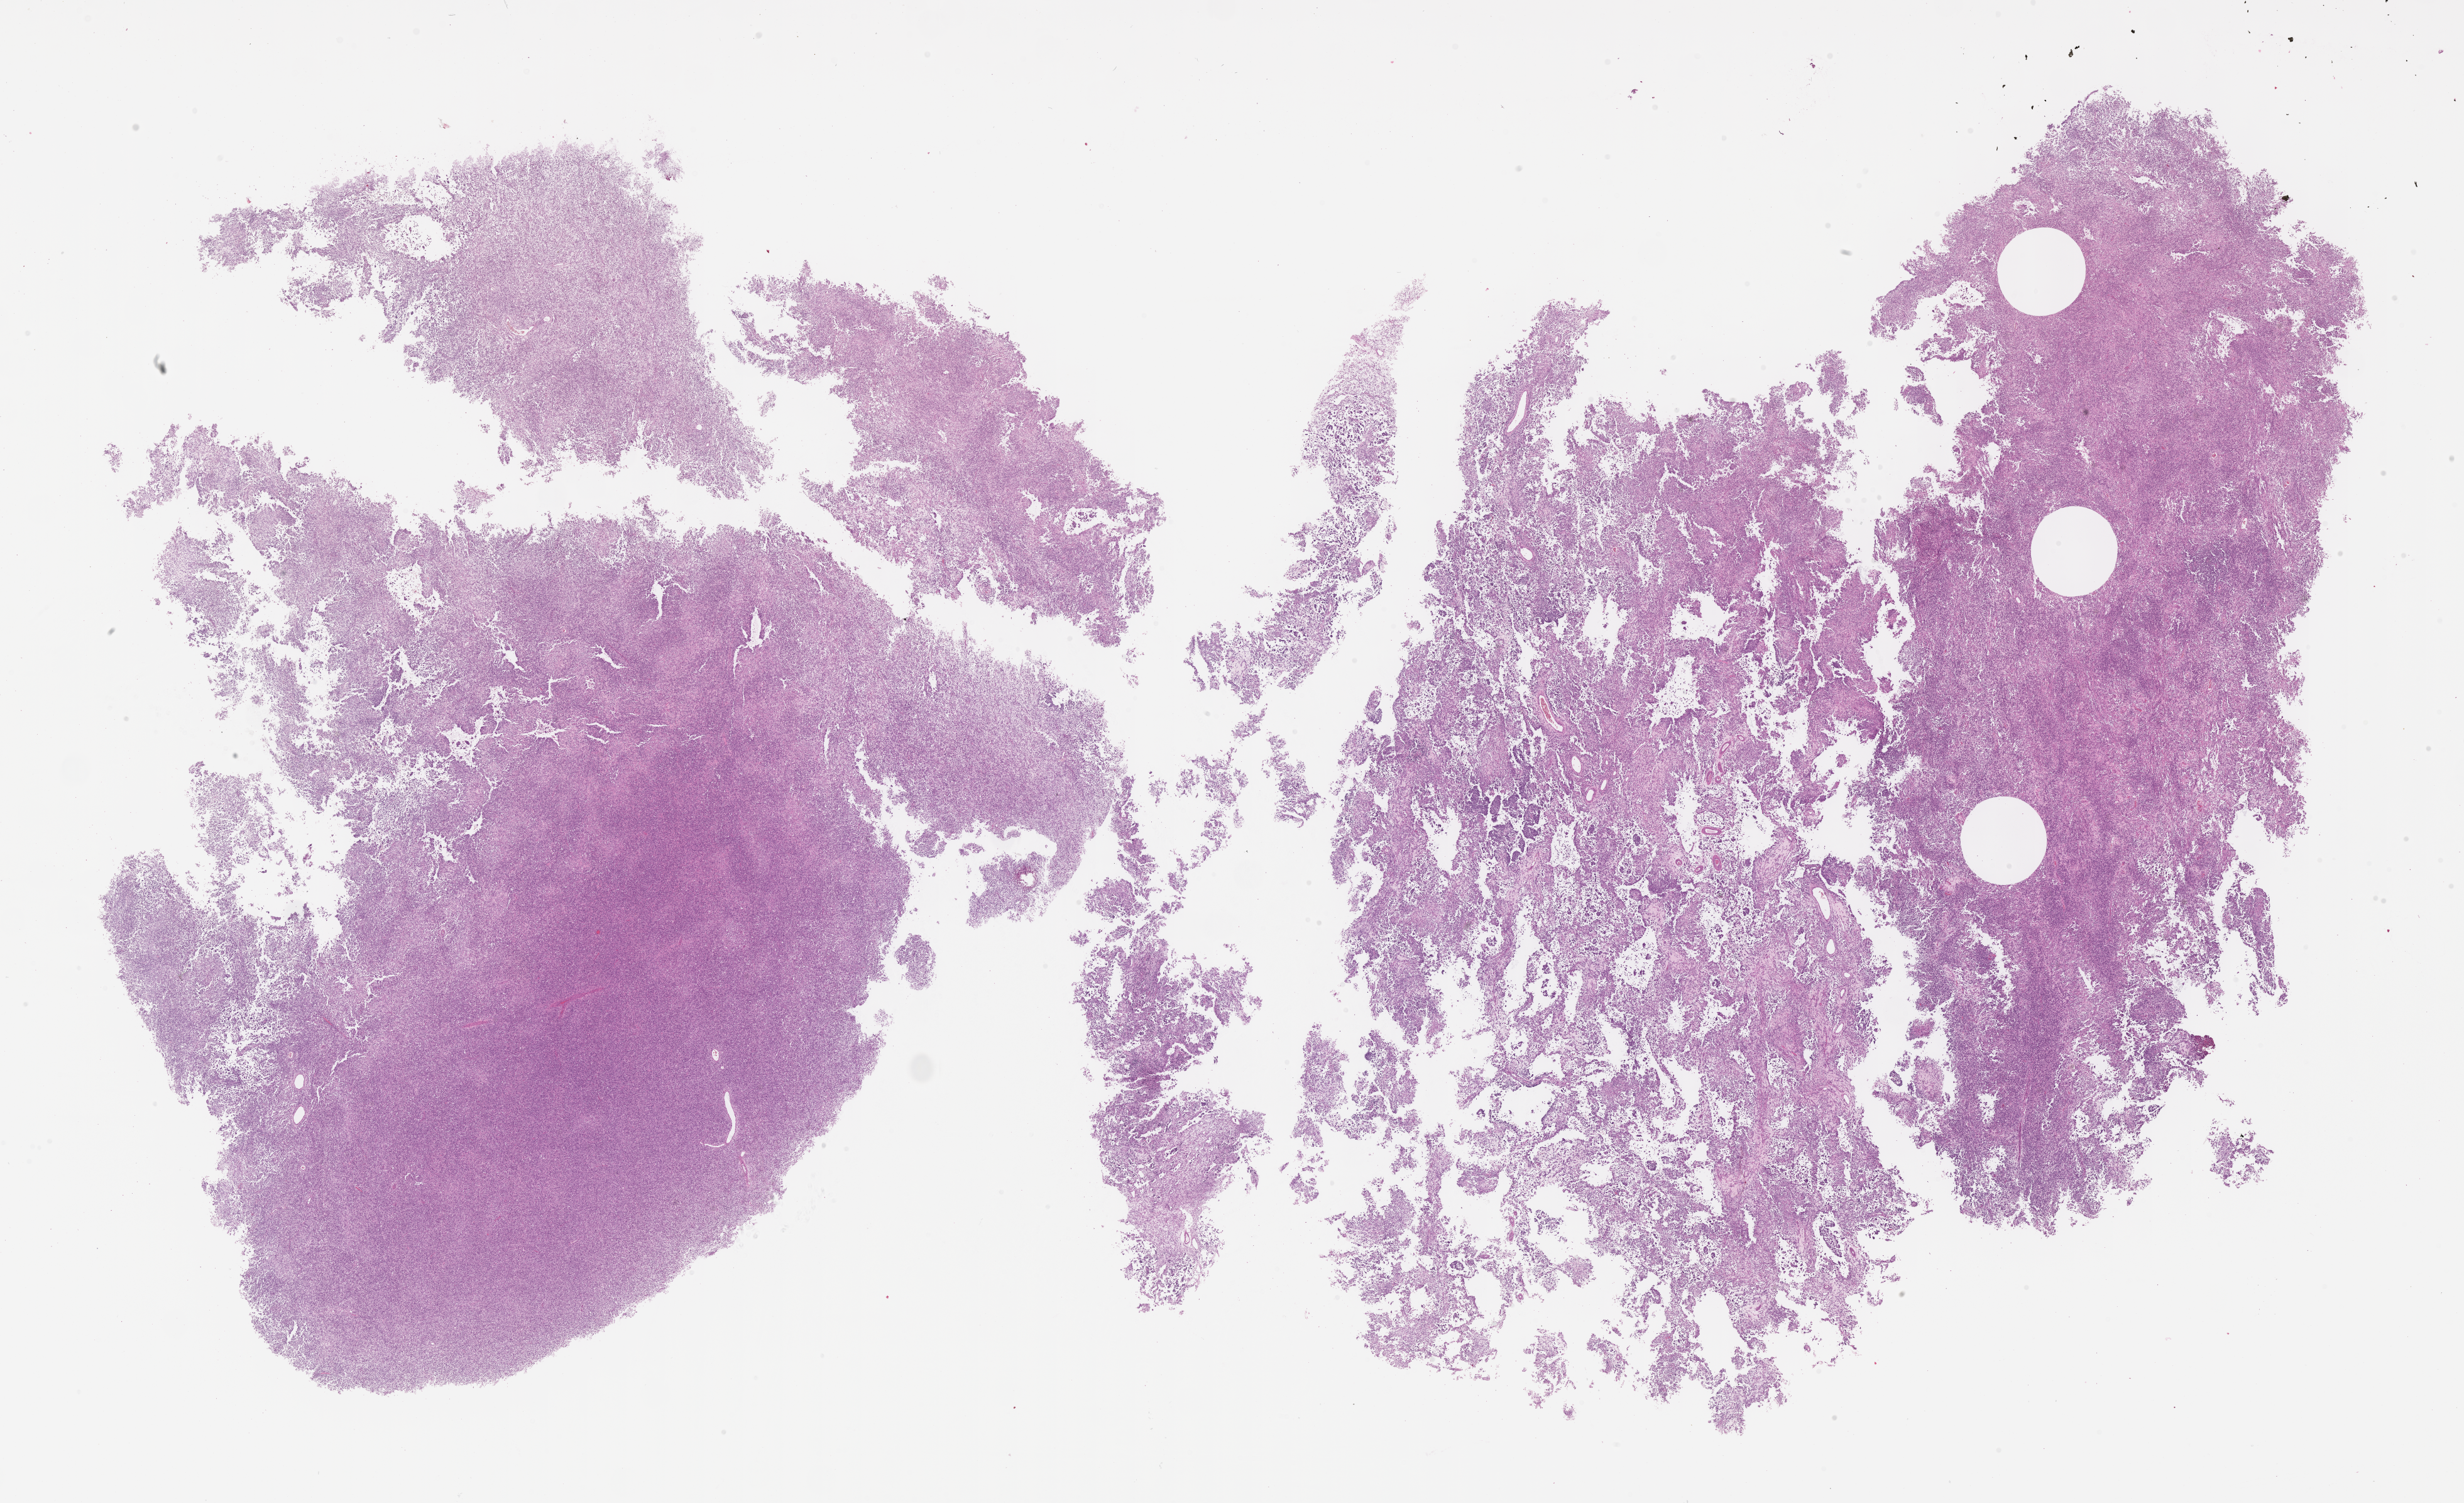
H&E whole-slide image of tumor tissue — low-resolution overview of the scanned area, about 31.7 x 19.3 mm, formalin-fixed paraffin-embedded section, sample anatomic site: thigh, right posterior. Patient: female, age 2.2 years at diagnosis.
* stage (as recorded): 3
* diagnosis: rhabdomyosarcoma; histological classification: alveolar rhabdomyosarcoma
* metastatic status at presentation (as recorded): non-metastatic